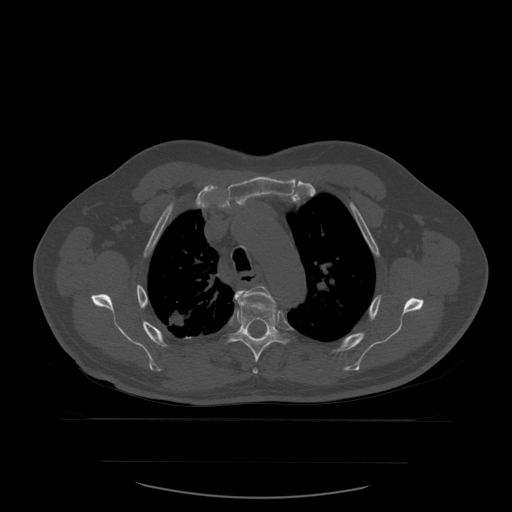
CT including the spine, one axial slice. Position 427 of 590 along the scan axis. Bone window (W 1800 / L 400 HU). 1.25 mm slice thickness. 512 × 512 image matrix, field of view 479 × 479 mm. Patient age 71 years. From the clinical record (not read from this slice): primary cancer: lung.
Outlined on this slice (semi-automatically segmented with operator editing):
- T4 vertebra: bounding box <238,286,277,374> (left, top, right, bottom; pixels)
- T5 vertebra: <219,292,297,363>
- T6 vertebra: <264,335,266,337>